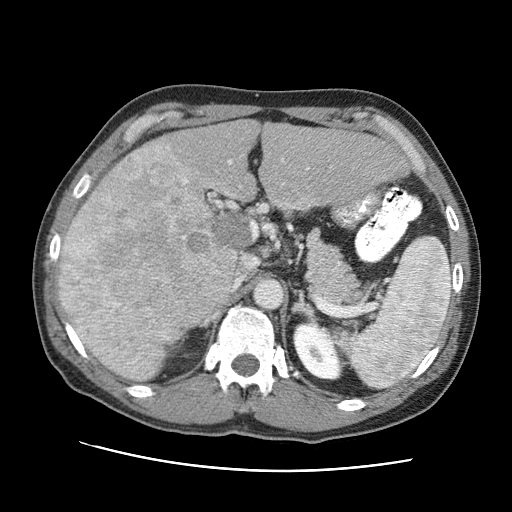
Contrast-enhanced abdominal CT (liver protocol), one axial slice. Position 51 of 95 along the scan axis. Reconstruction kernel STANDARD. 120 kVp. One of 2 acquisitions stored at this slice position. Soft-tissue window (W 400 / L 40 HU). 2.5 mm slice thickness. 512 × 512 image matrix, field of view 360 × 360 mm. From the clinical record (not read from this slice): diagnosis: hepatocellular carcinoma (patient treated with transarterial chemoembolisation; whether this scan precedes or follows treatment is not stated here); TNM stage (as recorded): Stage-IVA; Child-Pugh class: A.
Structures marked on this image (semi-automatic segmentation, software-assisted and operator-edited):
- abdominal aorta: bounding box (x1, y1, x2, y2) in pixels: (256, 281, 282, 308)
- liver parenchyma outside the tumour (the mass and vessels are separate outlines, so this box may not span the whole liver): (60, 120, 406, 321)
- mass: (58, 138, 249, 378)
- liver vessels: (73, 158, 310, 318)